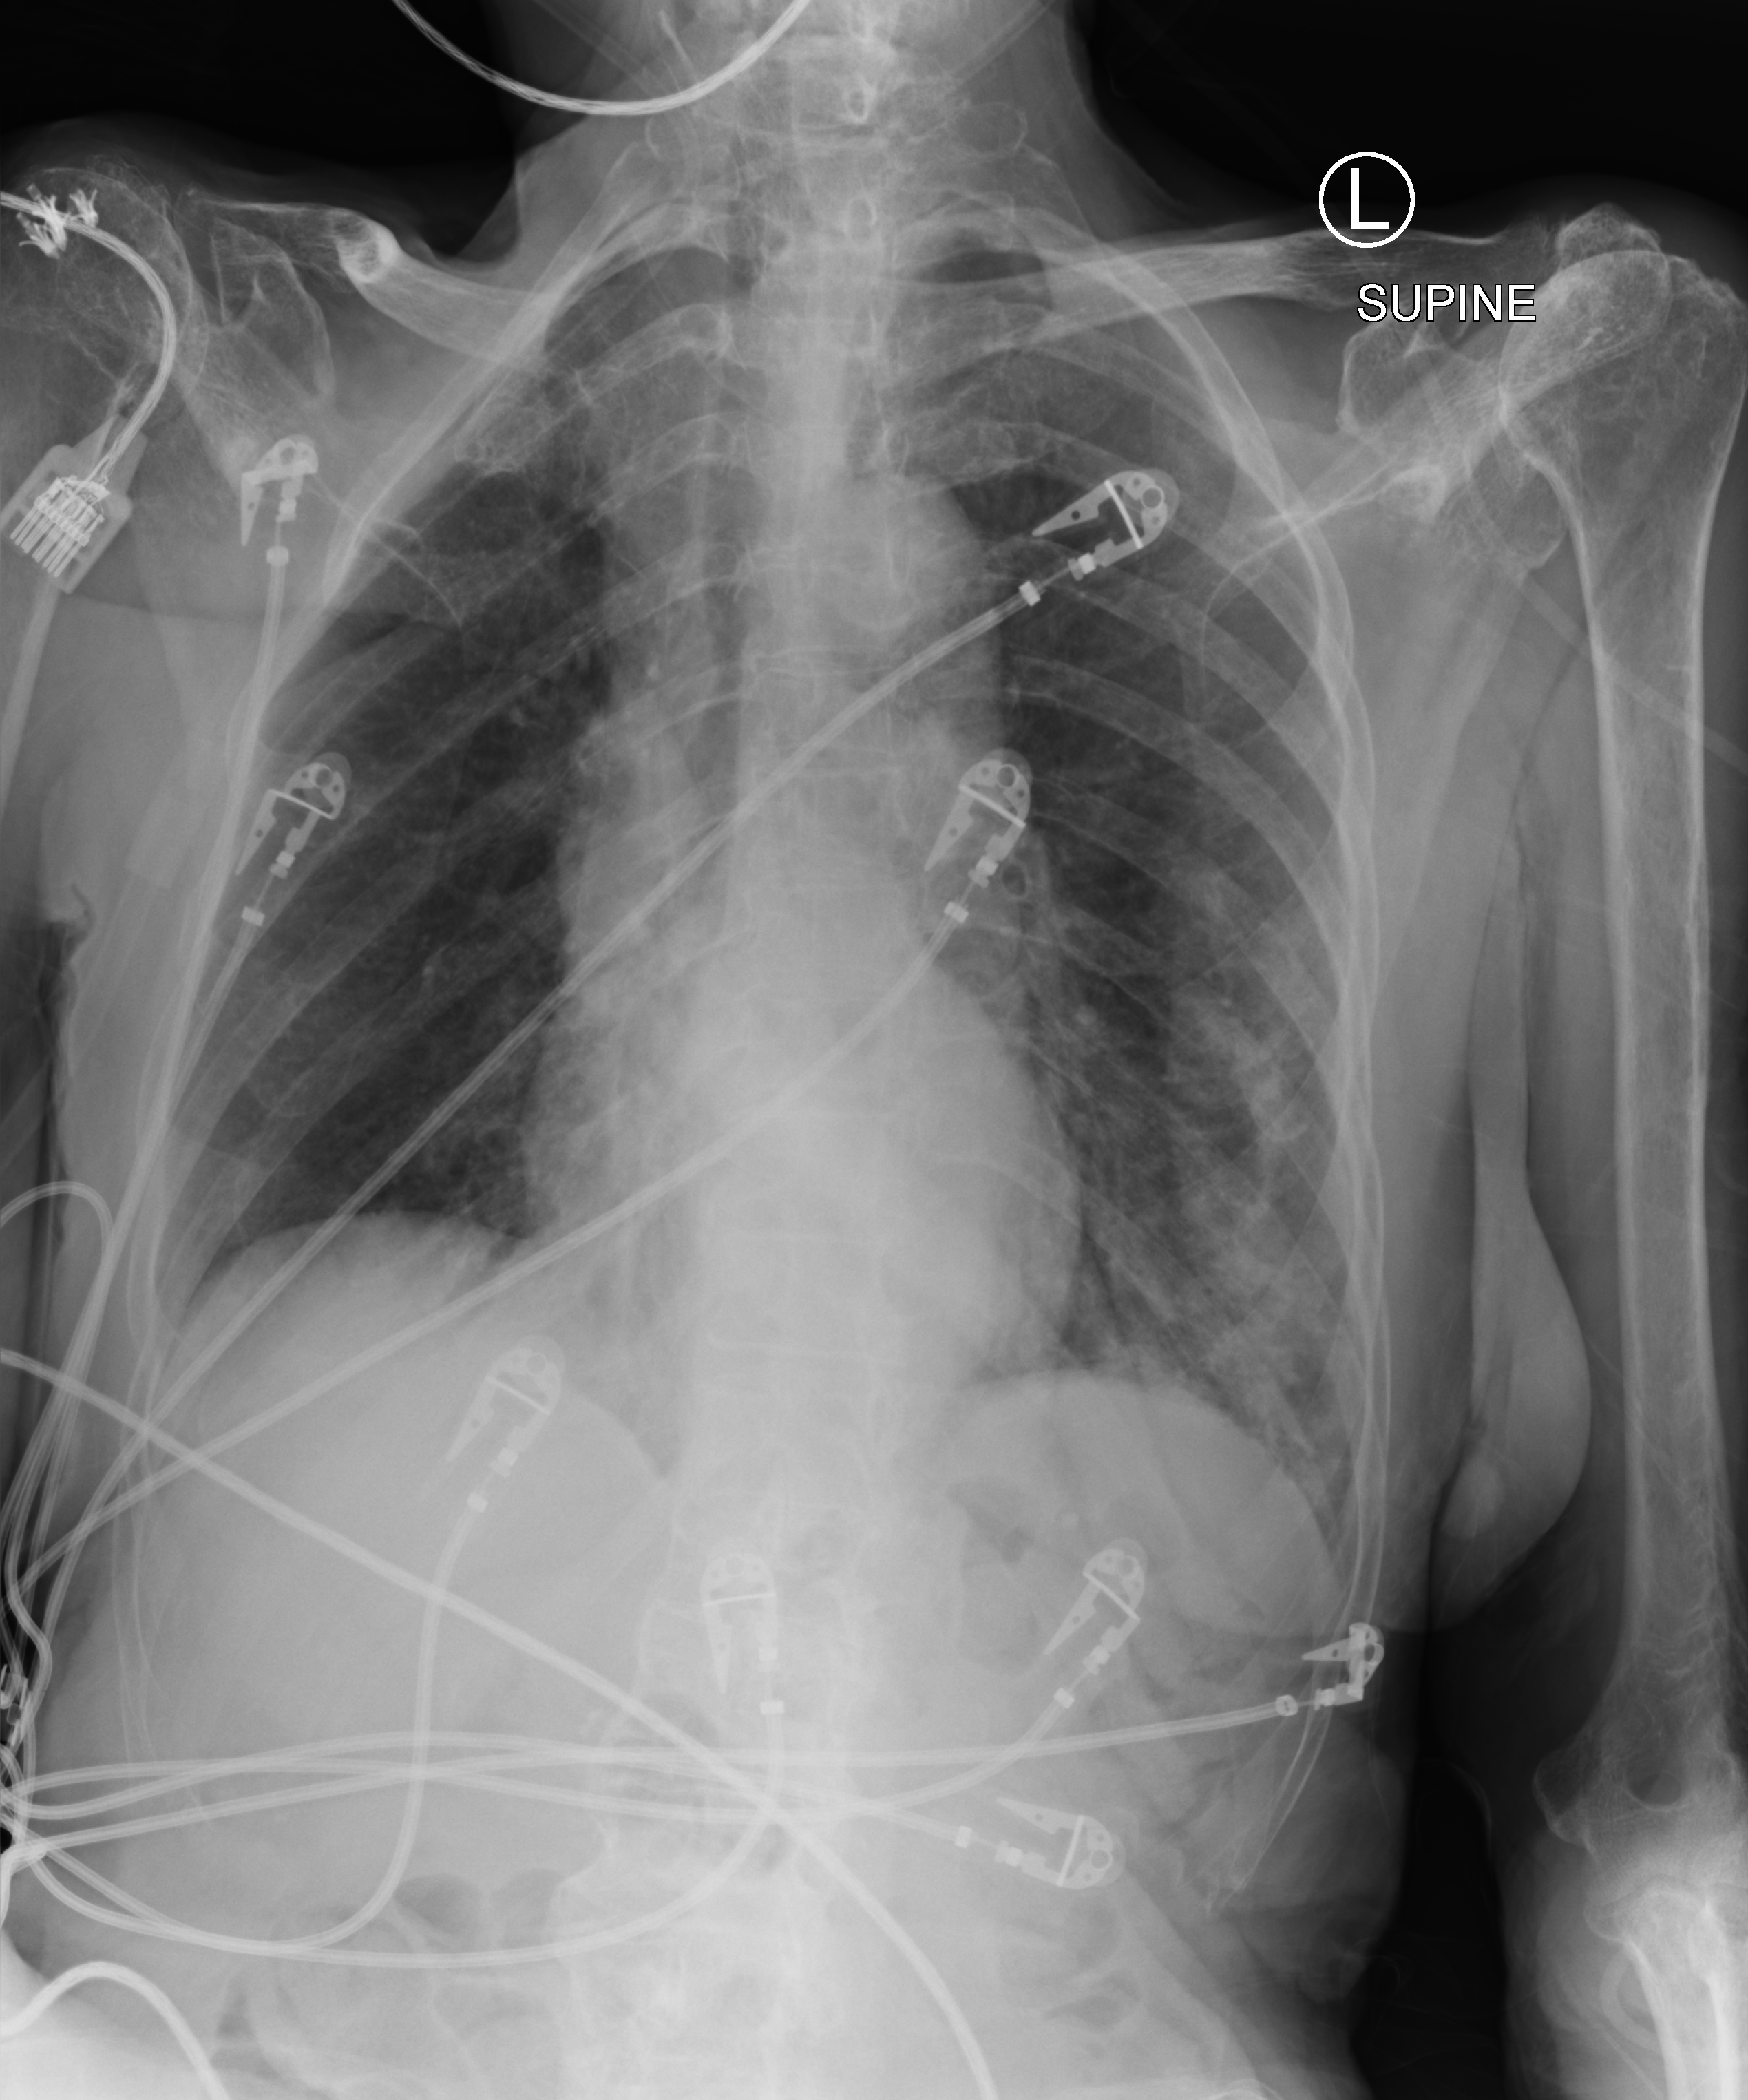
Portable chest radiograph; anteroposterior (AP) projection. Female patient hospitalised with COVID-19, age 75–90 years.
Hospital-stay facts (about this admission, not read from this image; timing relative to this image not recorded): mechanically ventilated during this hospital stay: no.